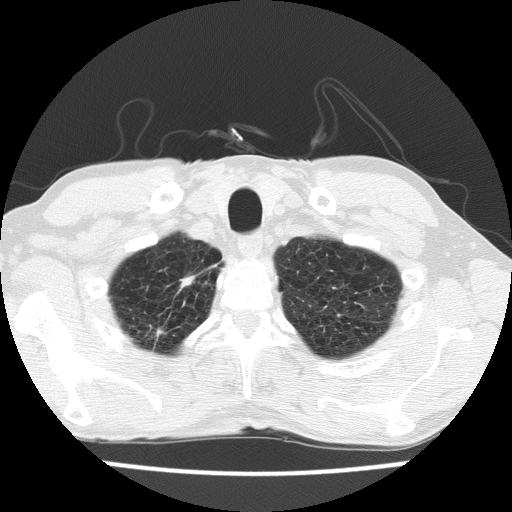
Chest CT (low-dose screening protocol), one axial image, second screening round (one year after baseline), lung window (W 1500 / L -600 HU), slice 18 of 175 in the series, 512 × 512 image matrix. Male participant, aged 63 years at enrolment.
Expert reader's lesion annotation, bounding box [x1, y1, x2, y2] px = [137, 263, 206, 332]. Screening reader's record for this exam: no non-calcified nodule ≥4 mm recorded. Official screen result: negative screen, minor abnormalities not suspicious for lung cancer. Lung cancer was diagnosed 390 days after this screen (after the third annual screen): adenocarcinoma, NOS, right upper lobe, moderately differentiated (G2), stage IIIB (AJCC 6th edition), 17 mm at pathology.